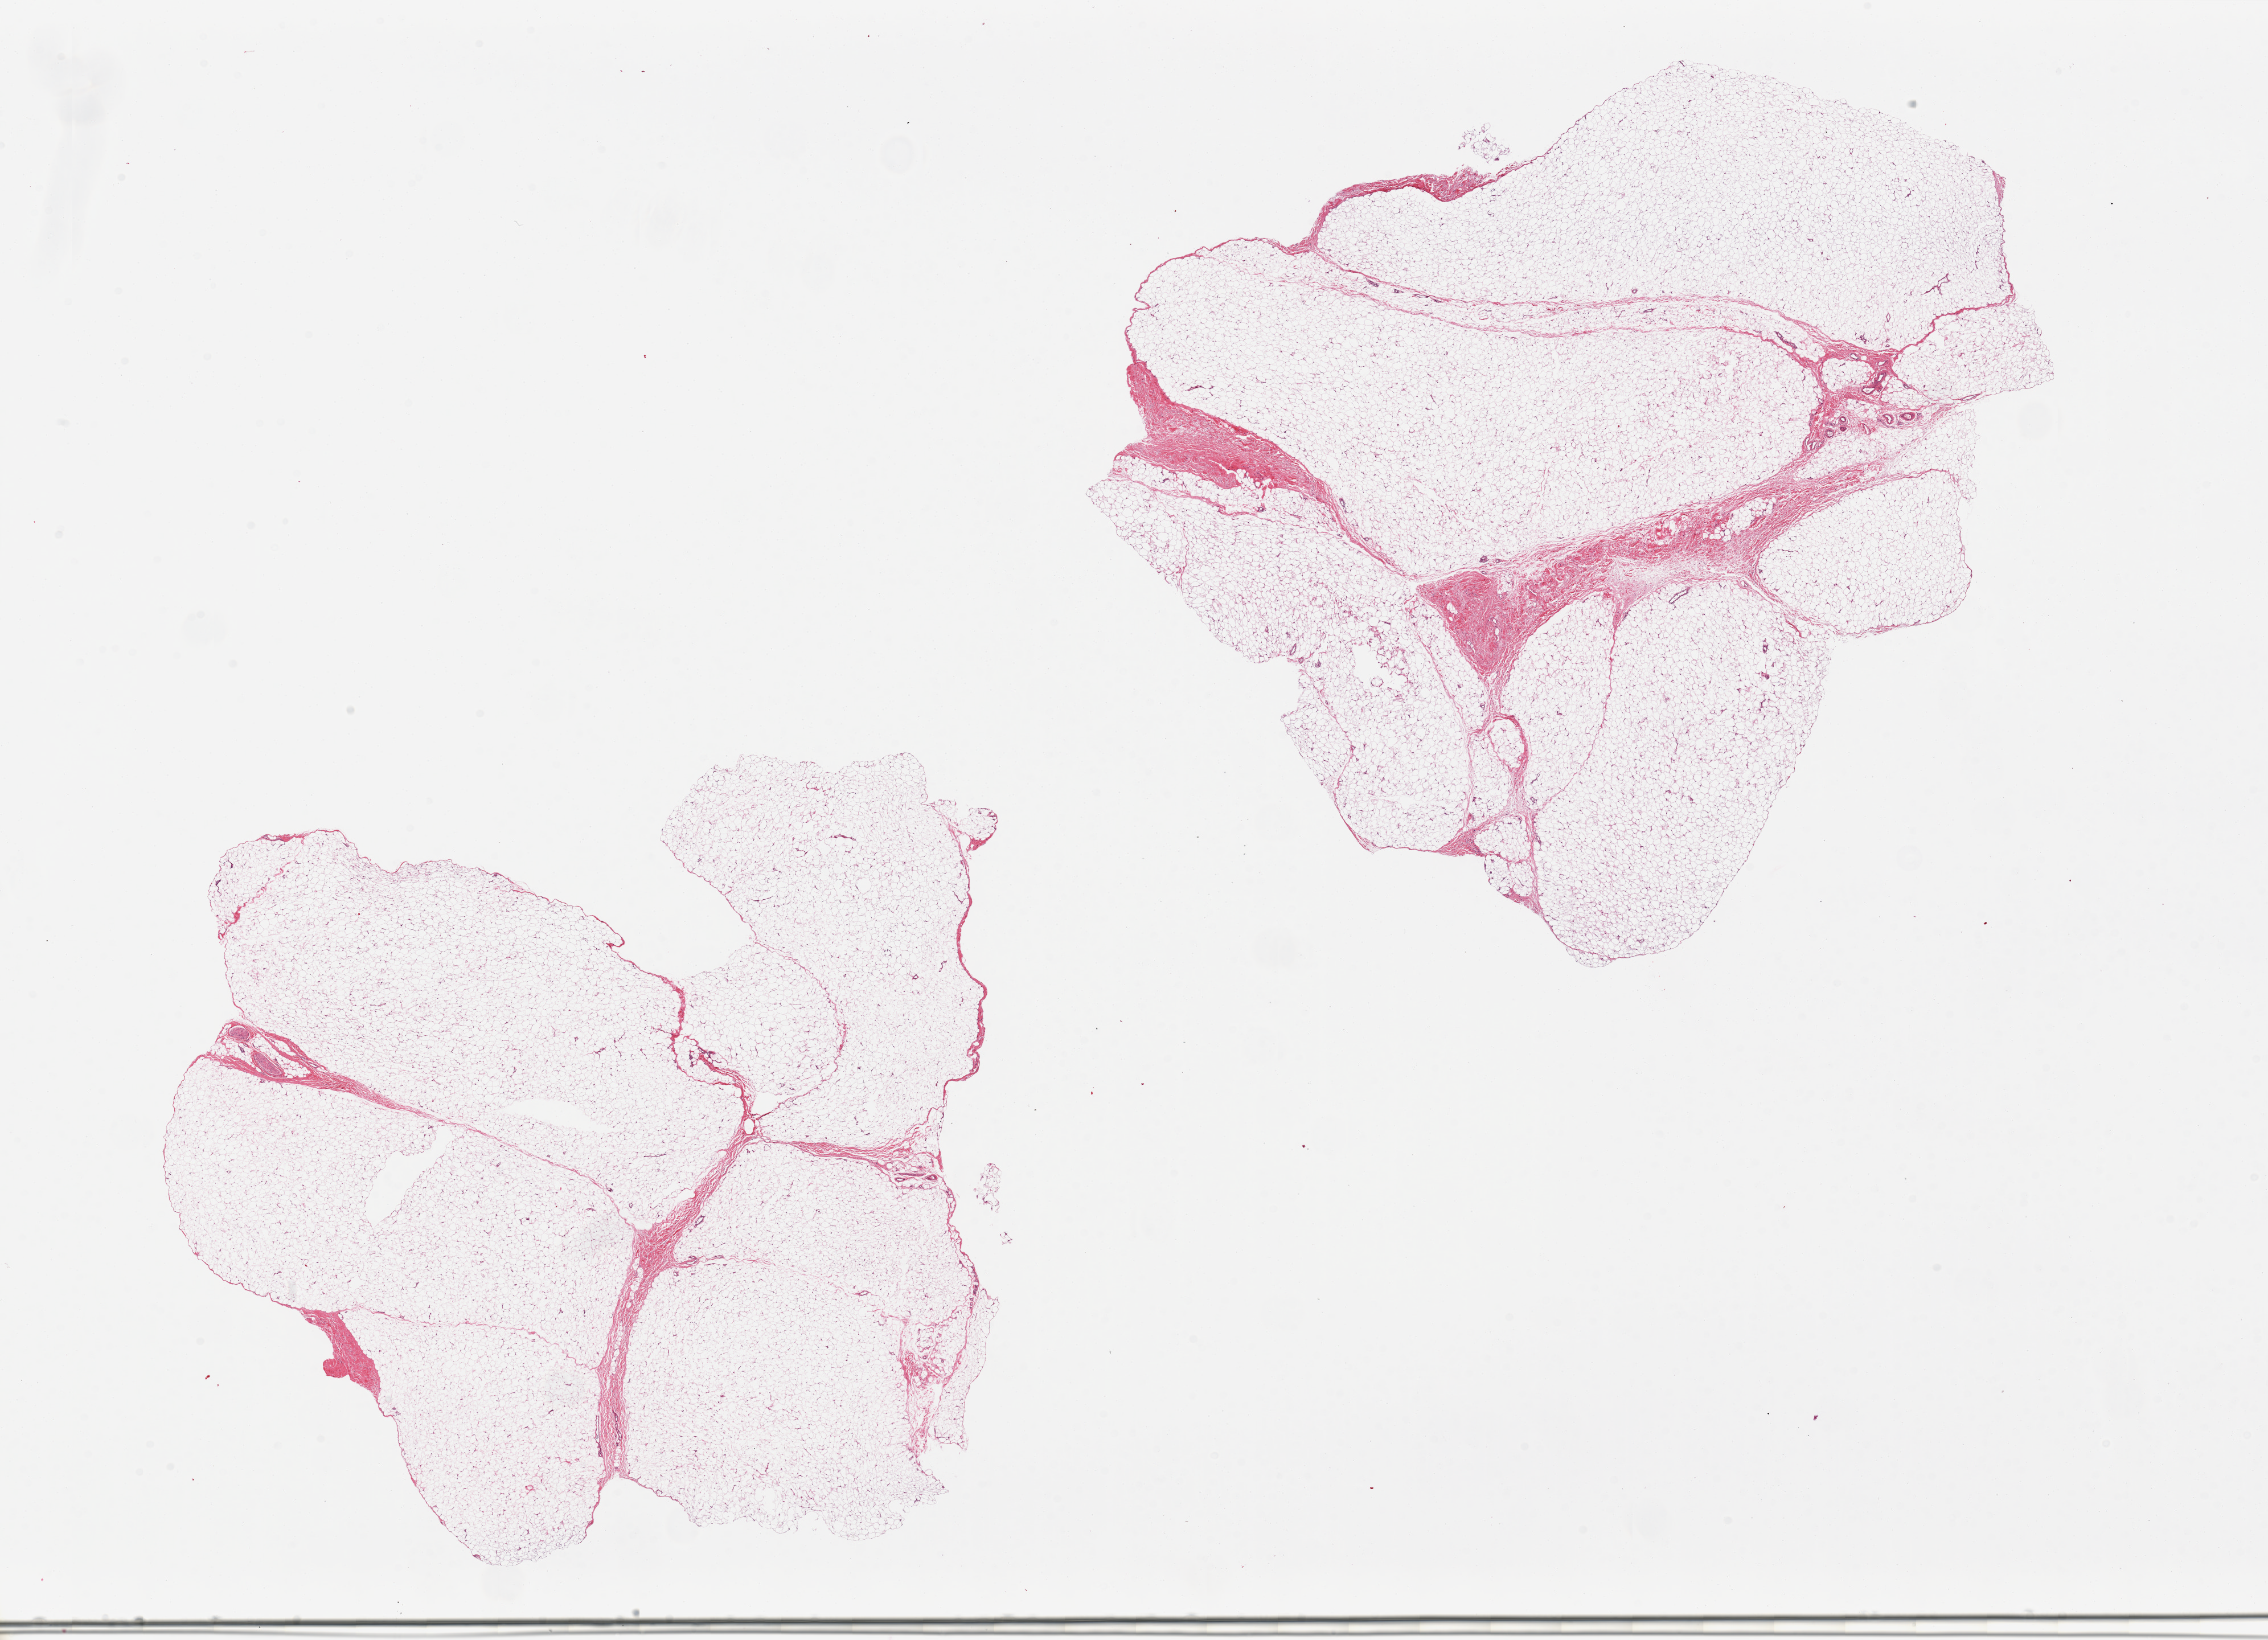
Whole-slide image, H&E stain, shown as a low-resolution overview of the whole scanned area (about 31.5 x 22.8 mm, from a 20x scan), PAXgene-fixed, paraffin-embedded tissue, section of adipose tissue (target tissue), tissue donor sample. Male donor.
Reviewer comment on this tissue sample: 2 pieces, ~10% of specimen is fibrous tissue (combined), few small nerves.